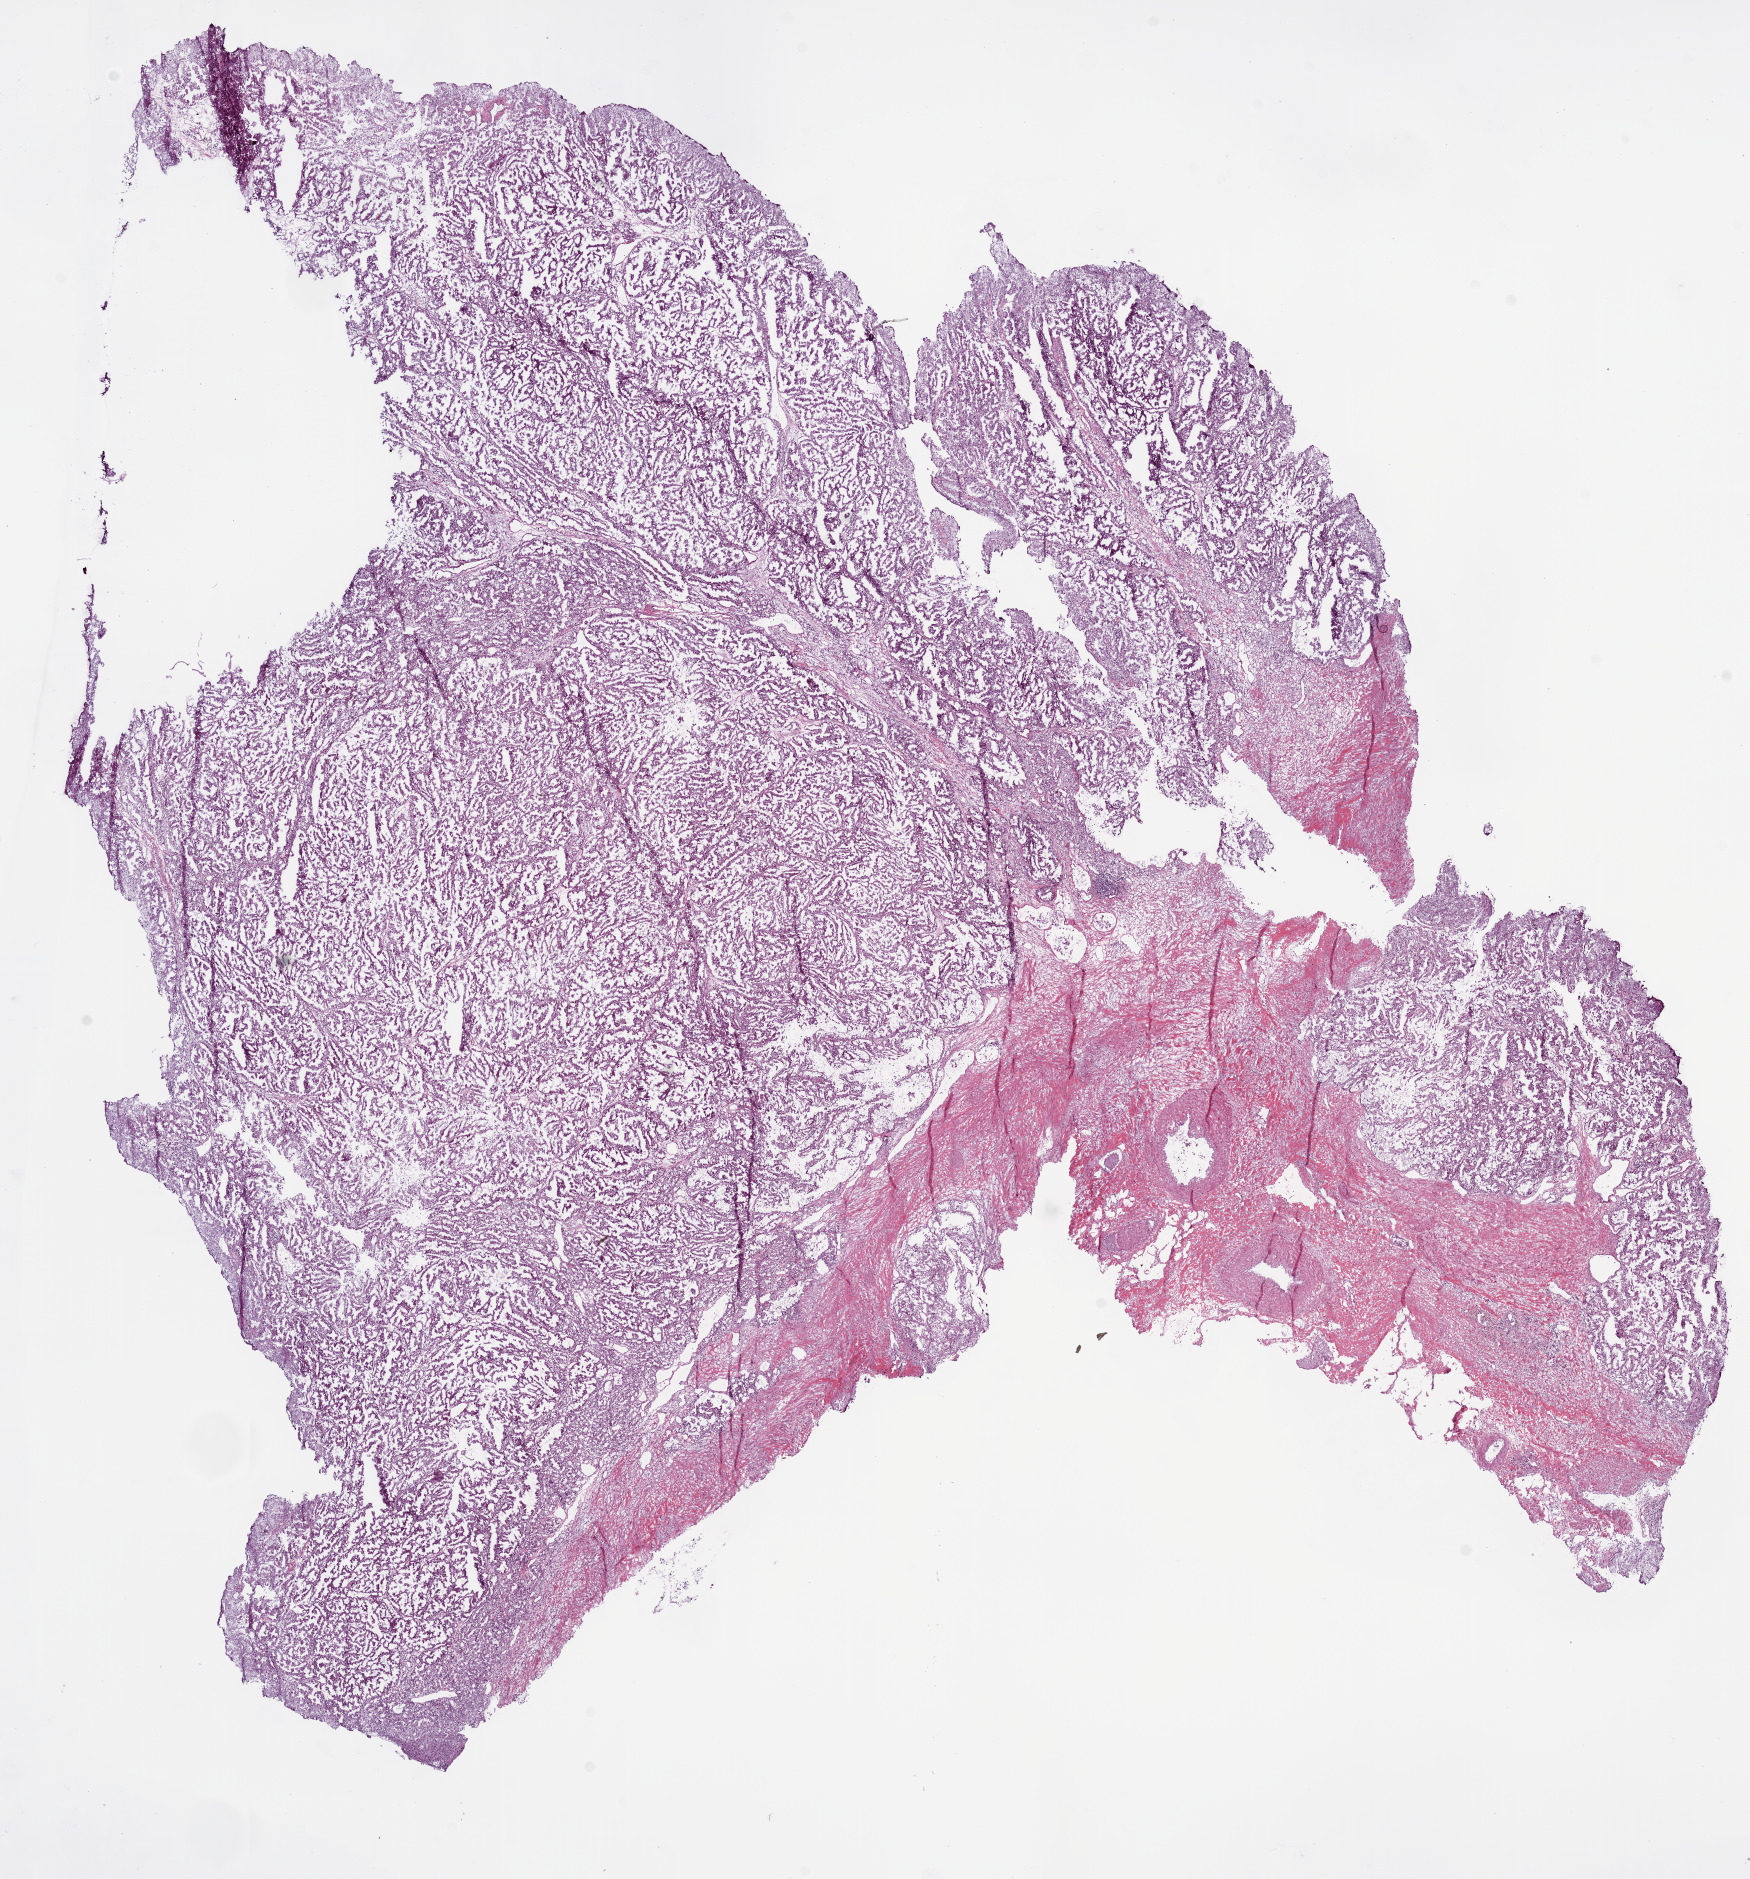
Hematoxylin and eosin (H&E) stained whole-slide image, a low-resolution overview of the entire scanned area, about 14.0 x 15.1 mm (slide scanned at 20x). Frozen section. Sample: primary tumour, kidney. Male patient; age at initial diagnosis 61 years.
Diagnosis: Clear cell adenocarcinoma, NOS.